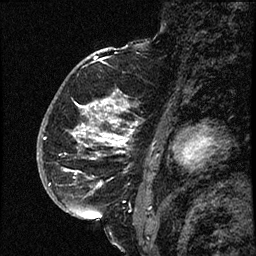
Breast MRI (dynamic contrast-enhanced), one sagittal slice; slice 45 of 66 in the series (ordered by position); dynamic contrast-enhanced study with each time point stored as its own series, time point 2 of 3 at this slice position (early post-contrast, ordered by acquisition time); 1.5 T; TE 4.2 ms, TR 17.6 ms; 256 × 256 image matrix, field of view 200 × 200 mm. Female patient. From the clinical record (not read from this slice): setting: breast cancer imaged before/during neoadjuvant chemotherapy; receptor status: HER2-positive.
Outlined on this slice (semi-automatic segmentation, software-assisted and operator-edited):
- analysis volume of interest (the breast-tissue region the enhancement analysis was run in; not a lesion): box from (x=52, y=69) to (x=143, y=209) px
- tumour enhancement mask (voxels above the 100 % enhancement threshold inside the analysis volume of interest): (x=73, y=98)–(x=136, y=186)